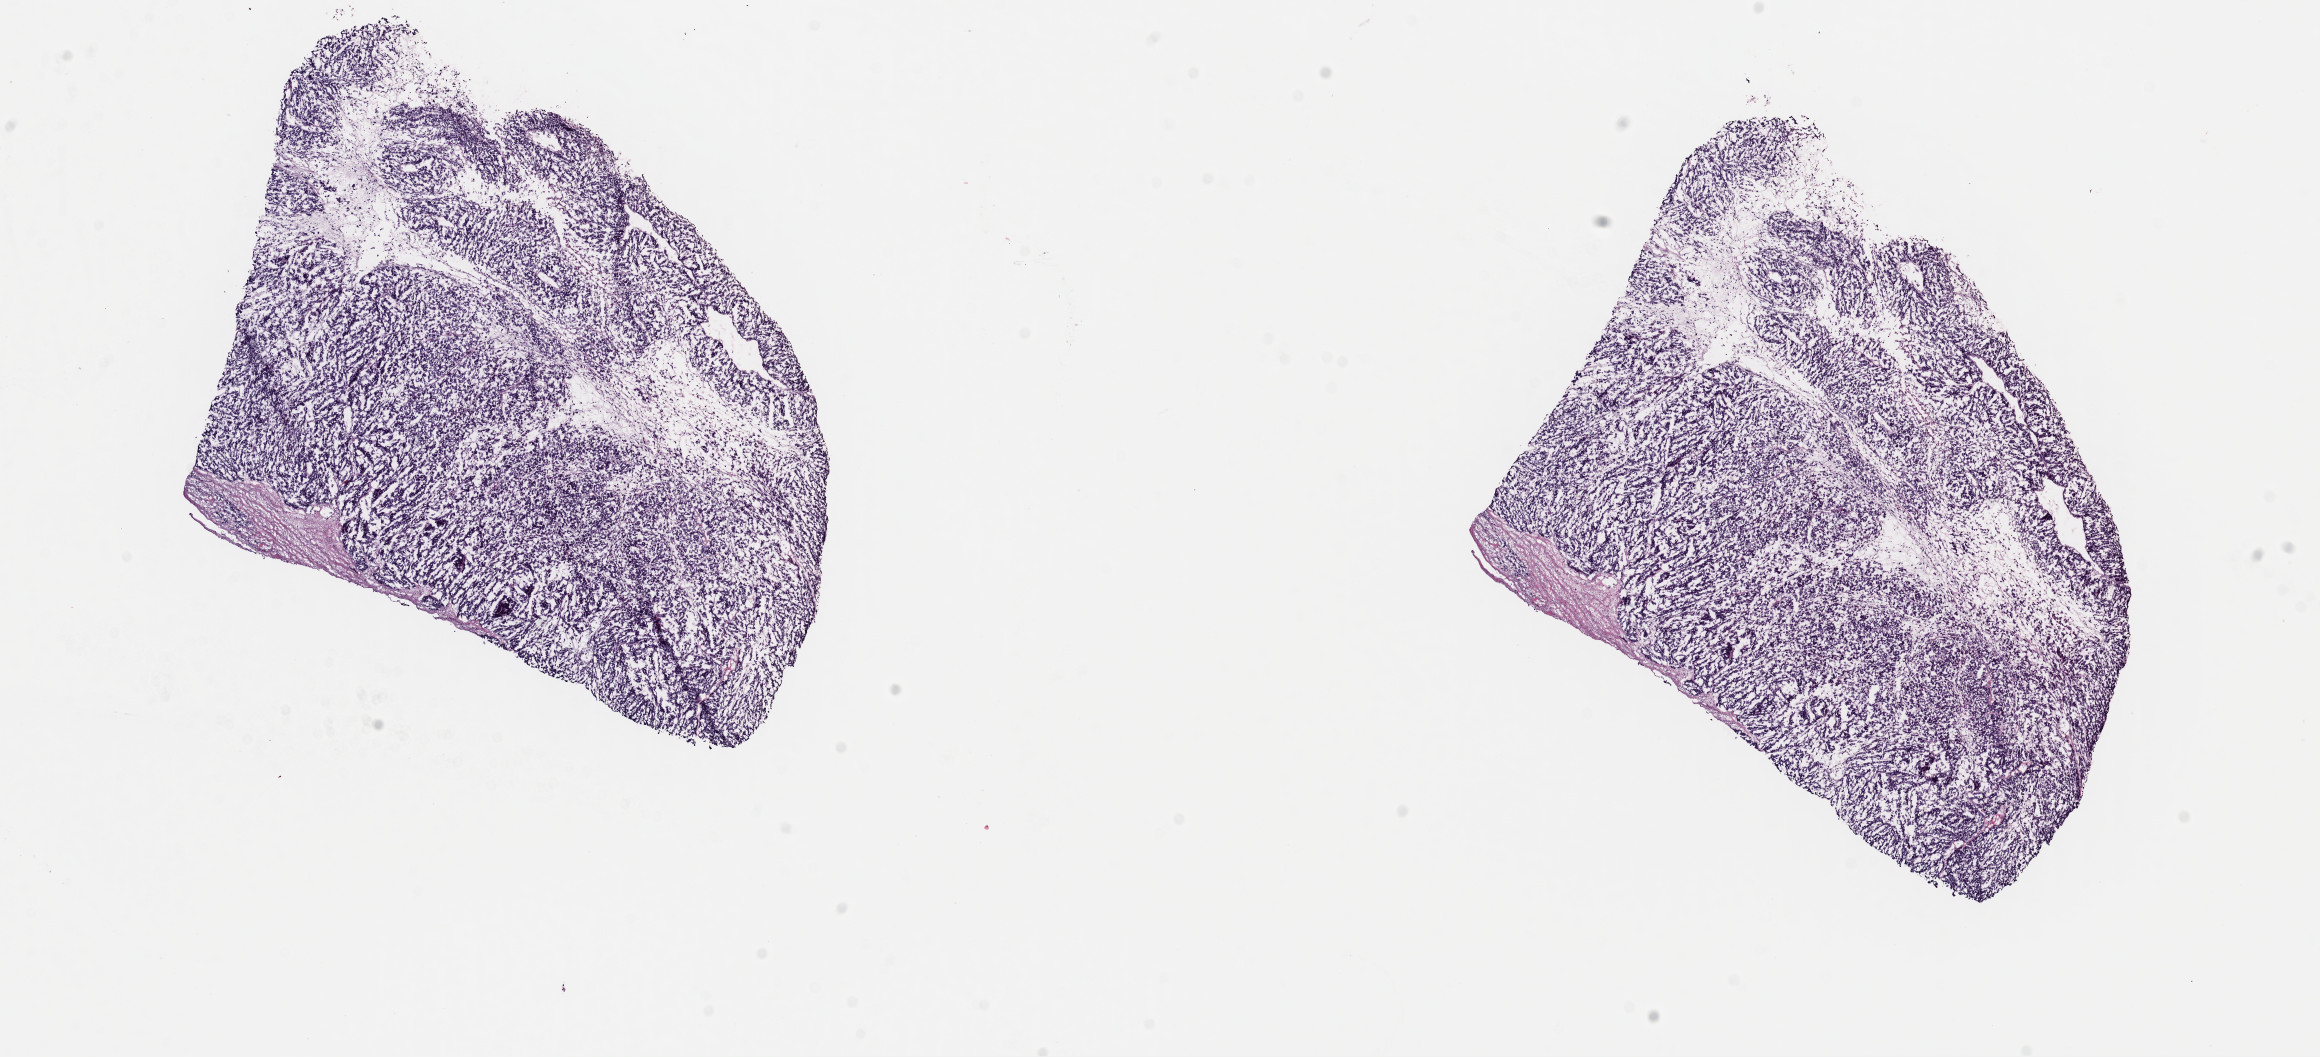
Digitized H&E-stained tissue section (whole slide), whole scanned area (about 18.3 x 8.3 mm, acquisition: 40x scan) shown as a low-resolution overview. Frozen section from the top of the tissue portion. Metastatic tumour sample, sampled site: skin. Male patient; age at initial diagnosis 51 years. Pathologist review of this section (percent, as recorded): tumour cells 85%, tumour nuclei 90%, normal cells 0%, stromal cells 10%, necrosis 5%. Inflammatory infiltration, as recorded: lymphocyte infiltration 3%, monocyte infiltration 1%, neutrophil infiltration 0%.
This section: metastatic tumour tissue. Patient diagnosis: Malignant melanoma, NOS.